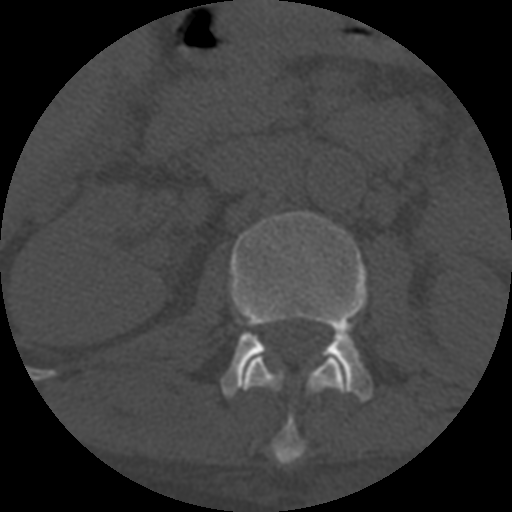
CT including the spine, one axial slice; position 271 of 708 along the scan axis; reconstruction kernel STANDARD; 120 kVp; one of 3 acquisitions stored at this slice position; bone window (W 1800 / L 400 HU); 1.25 mm slice thickness; 512 × 512 image matrix, field of view 160 × 160 mm. Patient age 55 years. From the clinical record (not read from this slice): primary cancer: colon.
Outlined on this slice (semi-automatically segmented with operator editing):
- L1 vertebra: box from (x=243, y=355) to (x=347, y=465) px
- L2 vertebra: (x=222, y=211)–(x=373, y=401)